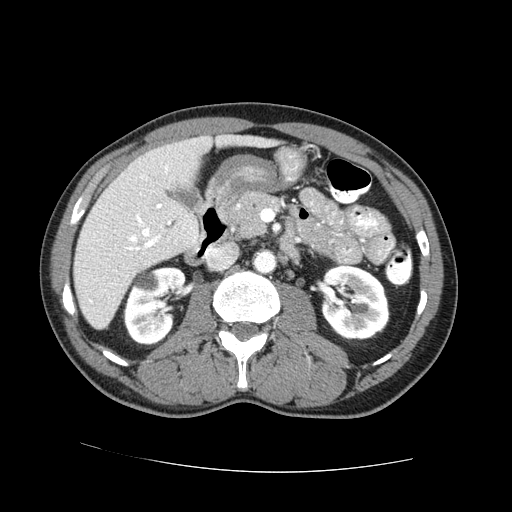
Contrast-enhanced abdominal CT (liver protocol), one axial slice. Position 28 of 73 along the scan axis. 100 kVp. One of 2 acquisitions stored at this slice position. Soft-tissue window (W 400 / L 40 HU). 2.5 mm slice thickness. 512 × 512 image matrix. From the clinical record (not read from this slice): diagnosis: hepatocellular carcinoma (patient treated with transarterial chemoembolisation; whether this scan precedes or follows treatment is not stated here); TNM stage (as recorded): Stage-IVA; Child-Pugh class: A; tumour nodularity: uninodular.
Structures marked on this image (semi-automatically segmented with operator editing):
- liver parenchyma outside the tumour (the mass and vessels are separate outlines, so this box may not span the whole liver): bounding box (x1, y1, x2, y2) in pixels: (74, 134, 272, 328)
- liver vessels: (90, 165, 171, 302)